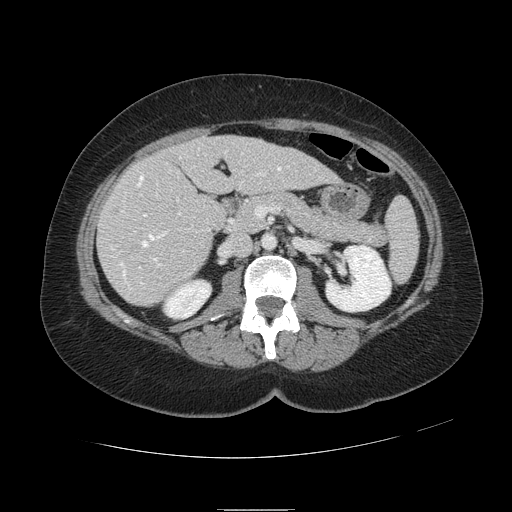
Contrast-enhanced abdominal CT, one axial slice; position 43 of 121 along the scan axis; 120 kVp; soft-tissue window (W 400 / L 40 HU); 2.5 mm slice thickness; 512 × 512 image matrix. Female patient, age 52 years. Case-level facts recorded for this patient, not image findings: diagnosis: colorectal cancer liver metastases, imaged before liver resection.
Structures marked on this image (expert manual segmentation):
- hepatic veins: bounding box [x1, y1, x2, y2] px = [111, 151, 281, 284]
- liver: [98, 136, 336, 306]
- planned liver remnant (the part of the liver to remain after resection): [177, 136, 337, 195]
- portal vein (with intrahepatic branches): [139, 199, 181, 269]